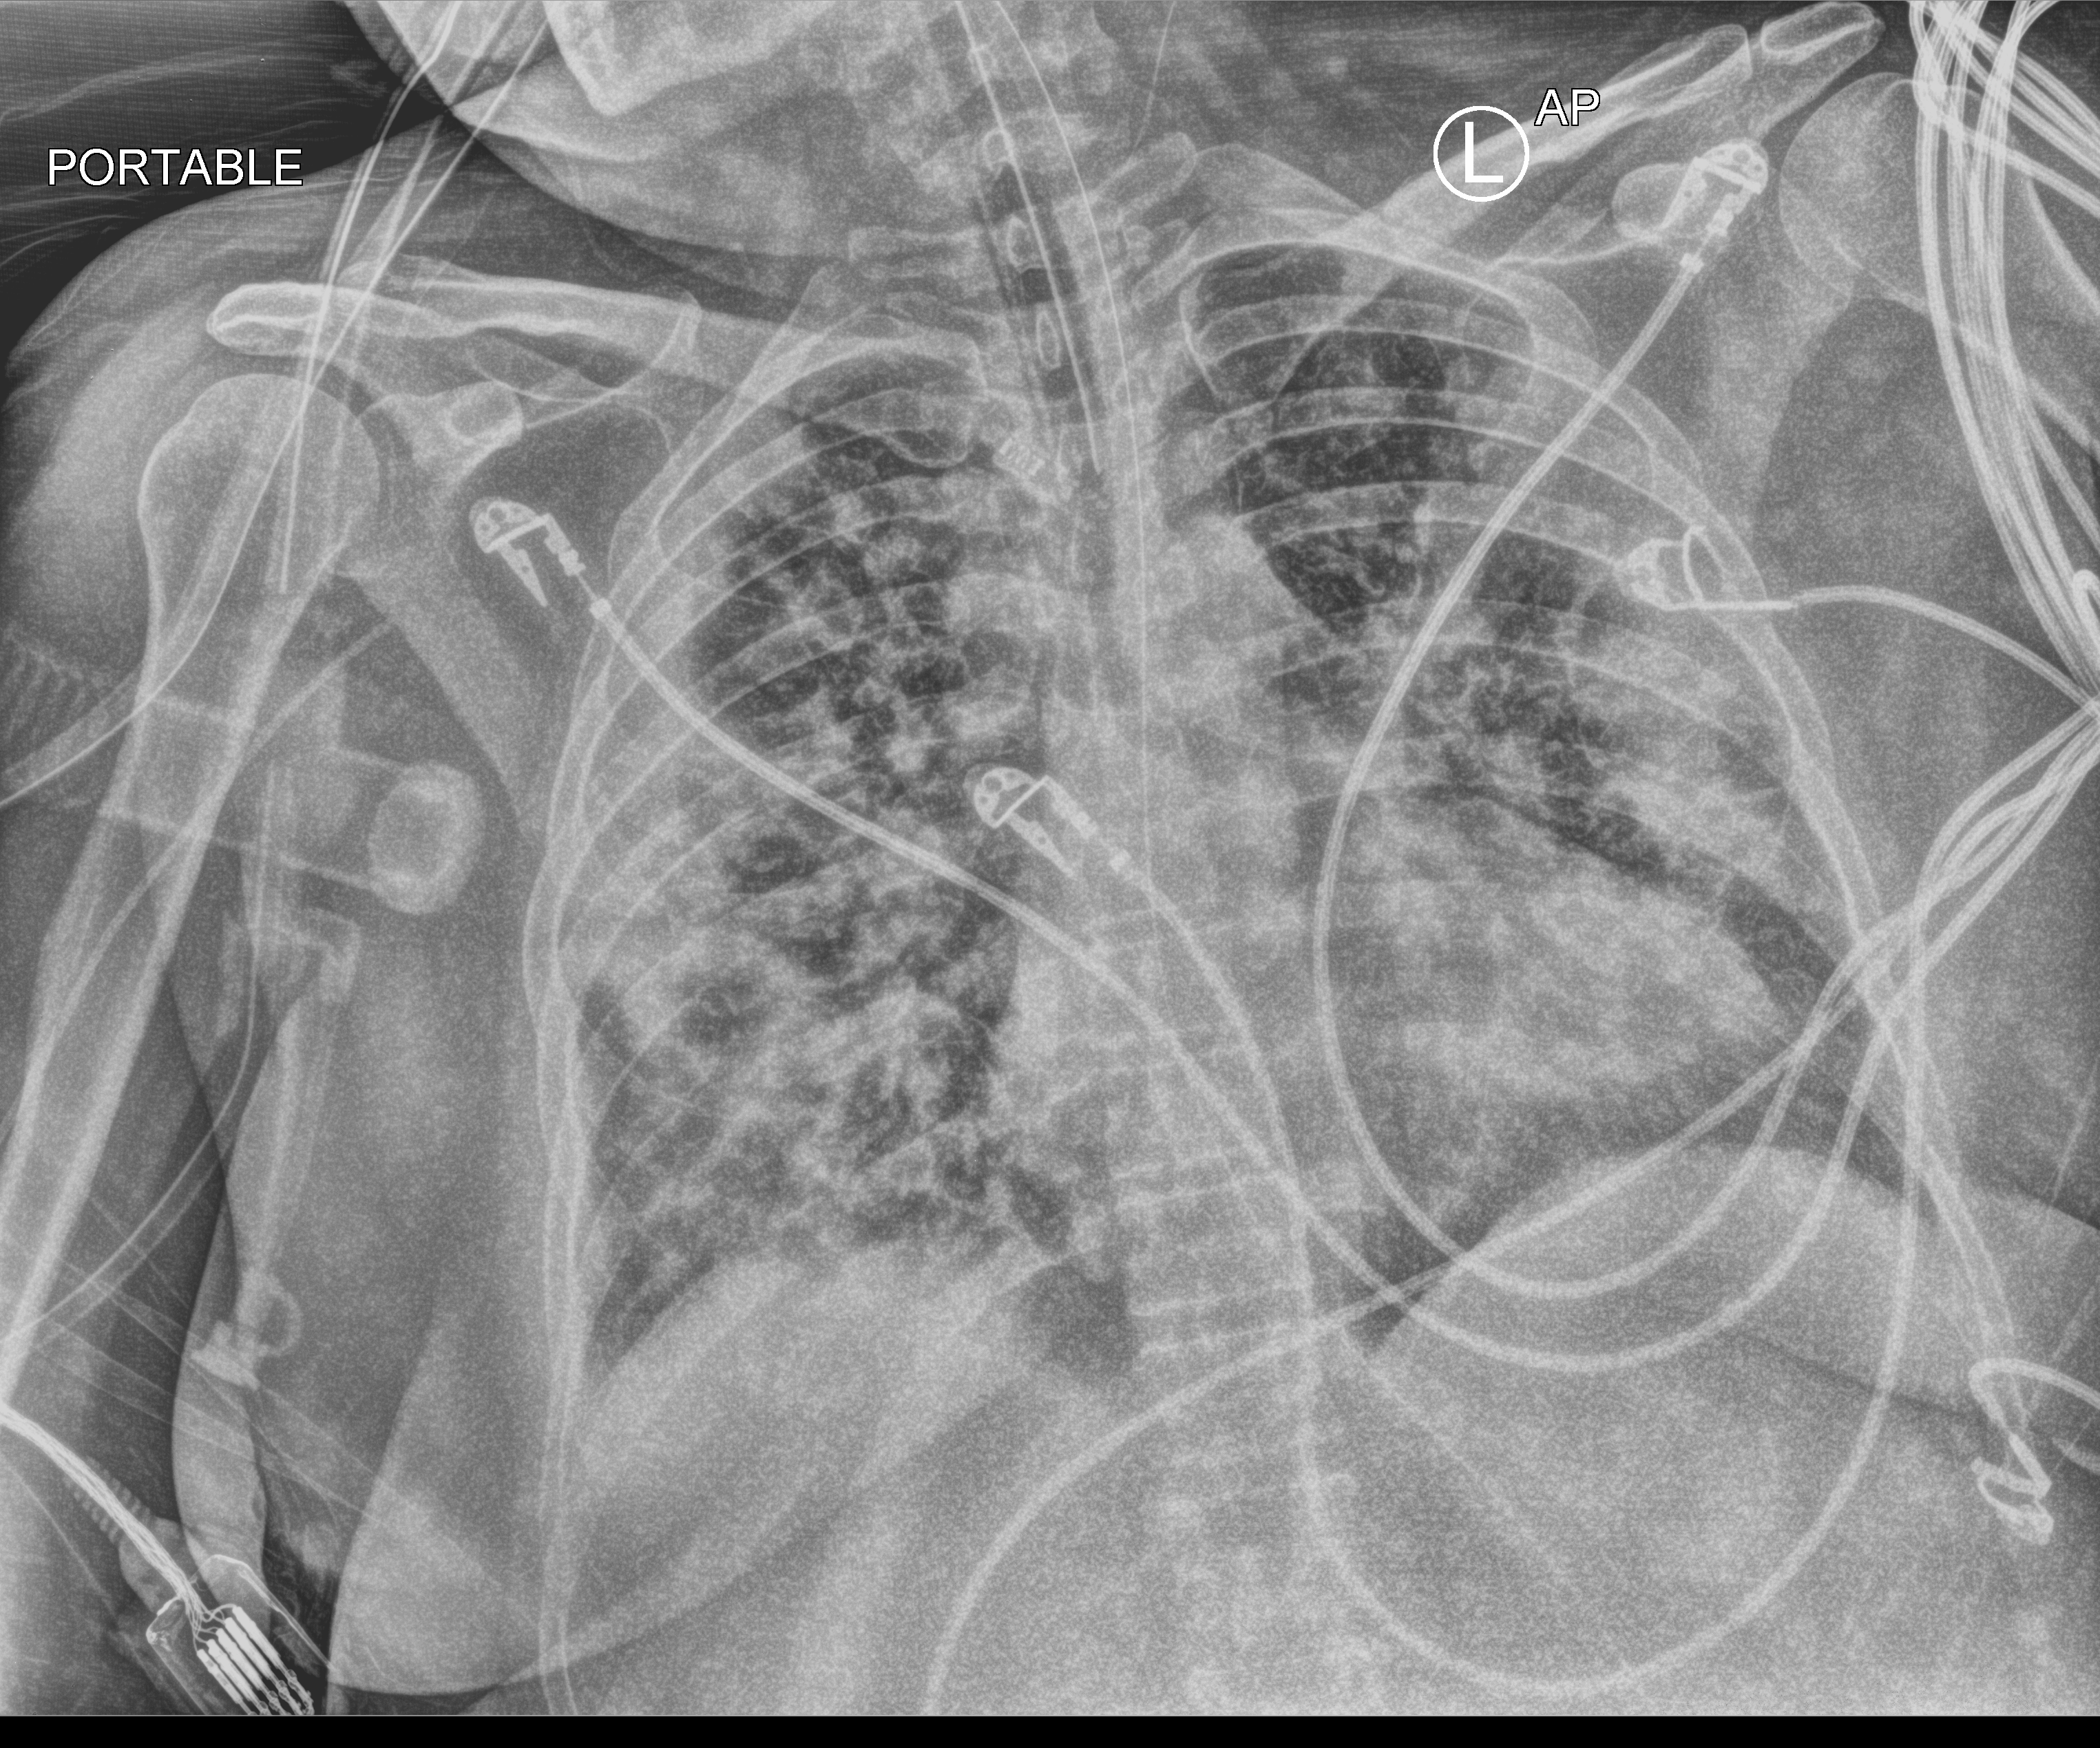
Bedside chest radiograph (computed radiography). Patient hospitalised with COVID-19; female, aged 18–59 years.
Admission-level facts for this patient (not findings on this image; timing relative to this image not recorded): length of hospital stay: 31 days; chronic kidney disease (admission record): no; other chronic lung disease (admission record): no.